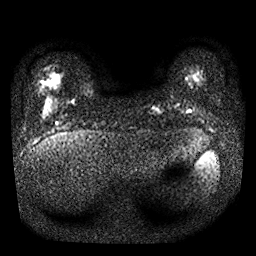
Breast MRI, one axial slice. Slice 2 of 24 in the series (ordered by position). Diffusion-weighted series; image 2 of 4 stored at this slice position (different b-values; order by instance number). 1.5 T. 256 × 256 image matrix, field of view 300 × 300 mm. Female patient.
Structures marked on this image (expert manual segmentation):
- tumour on diffusion-weighted imaging: bounding box <153,107,158,110> (left, top, right, bottom; pixels)